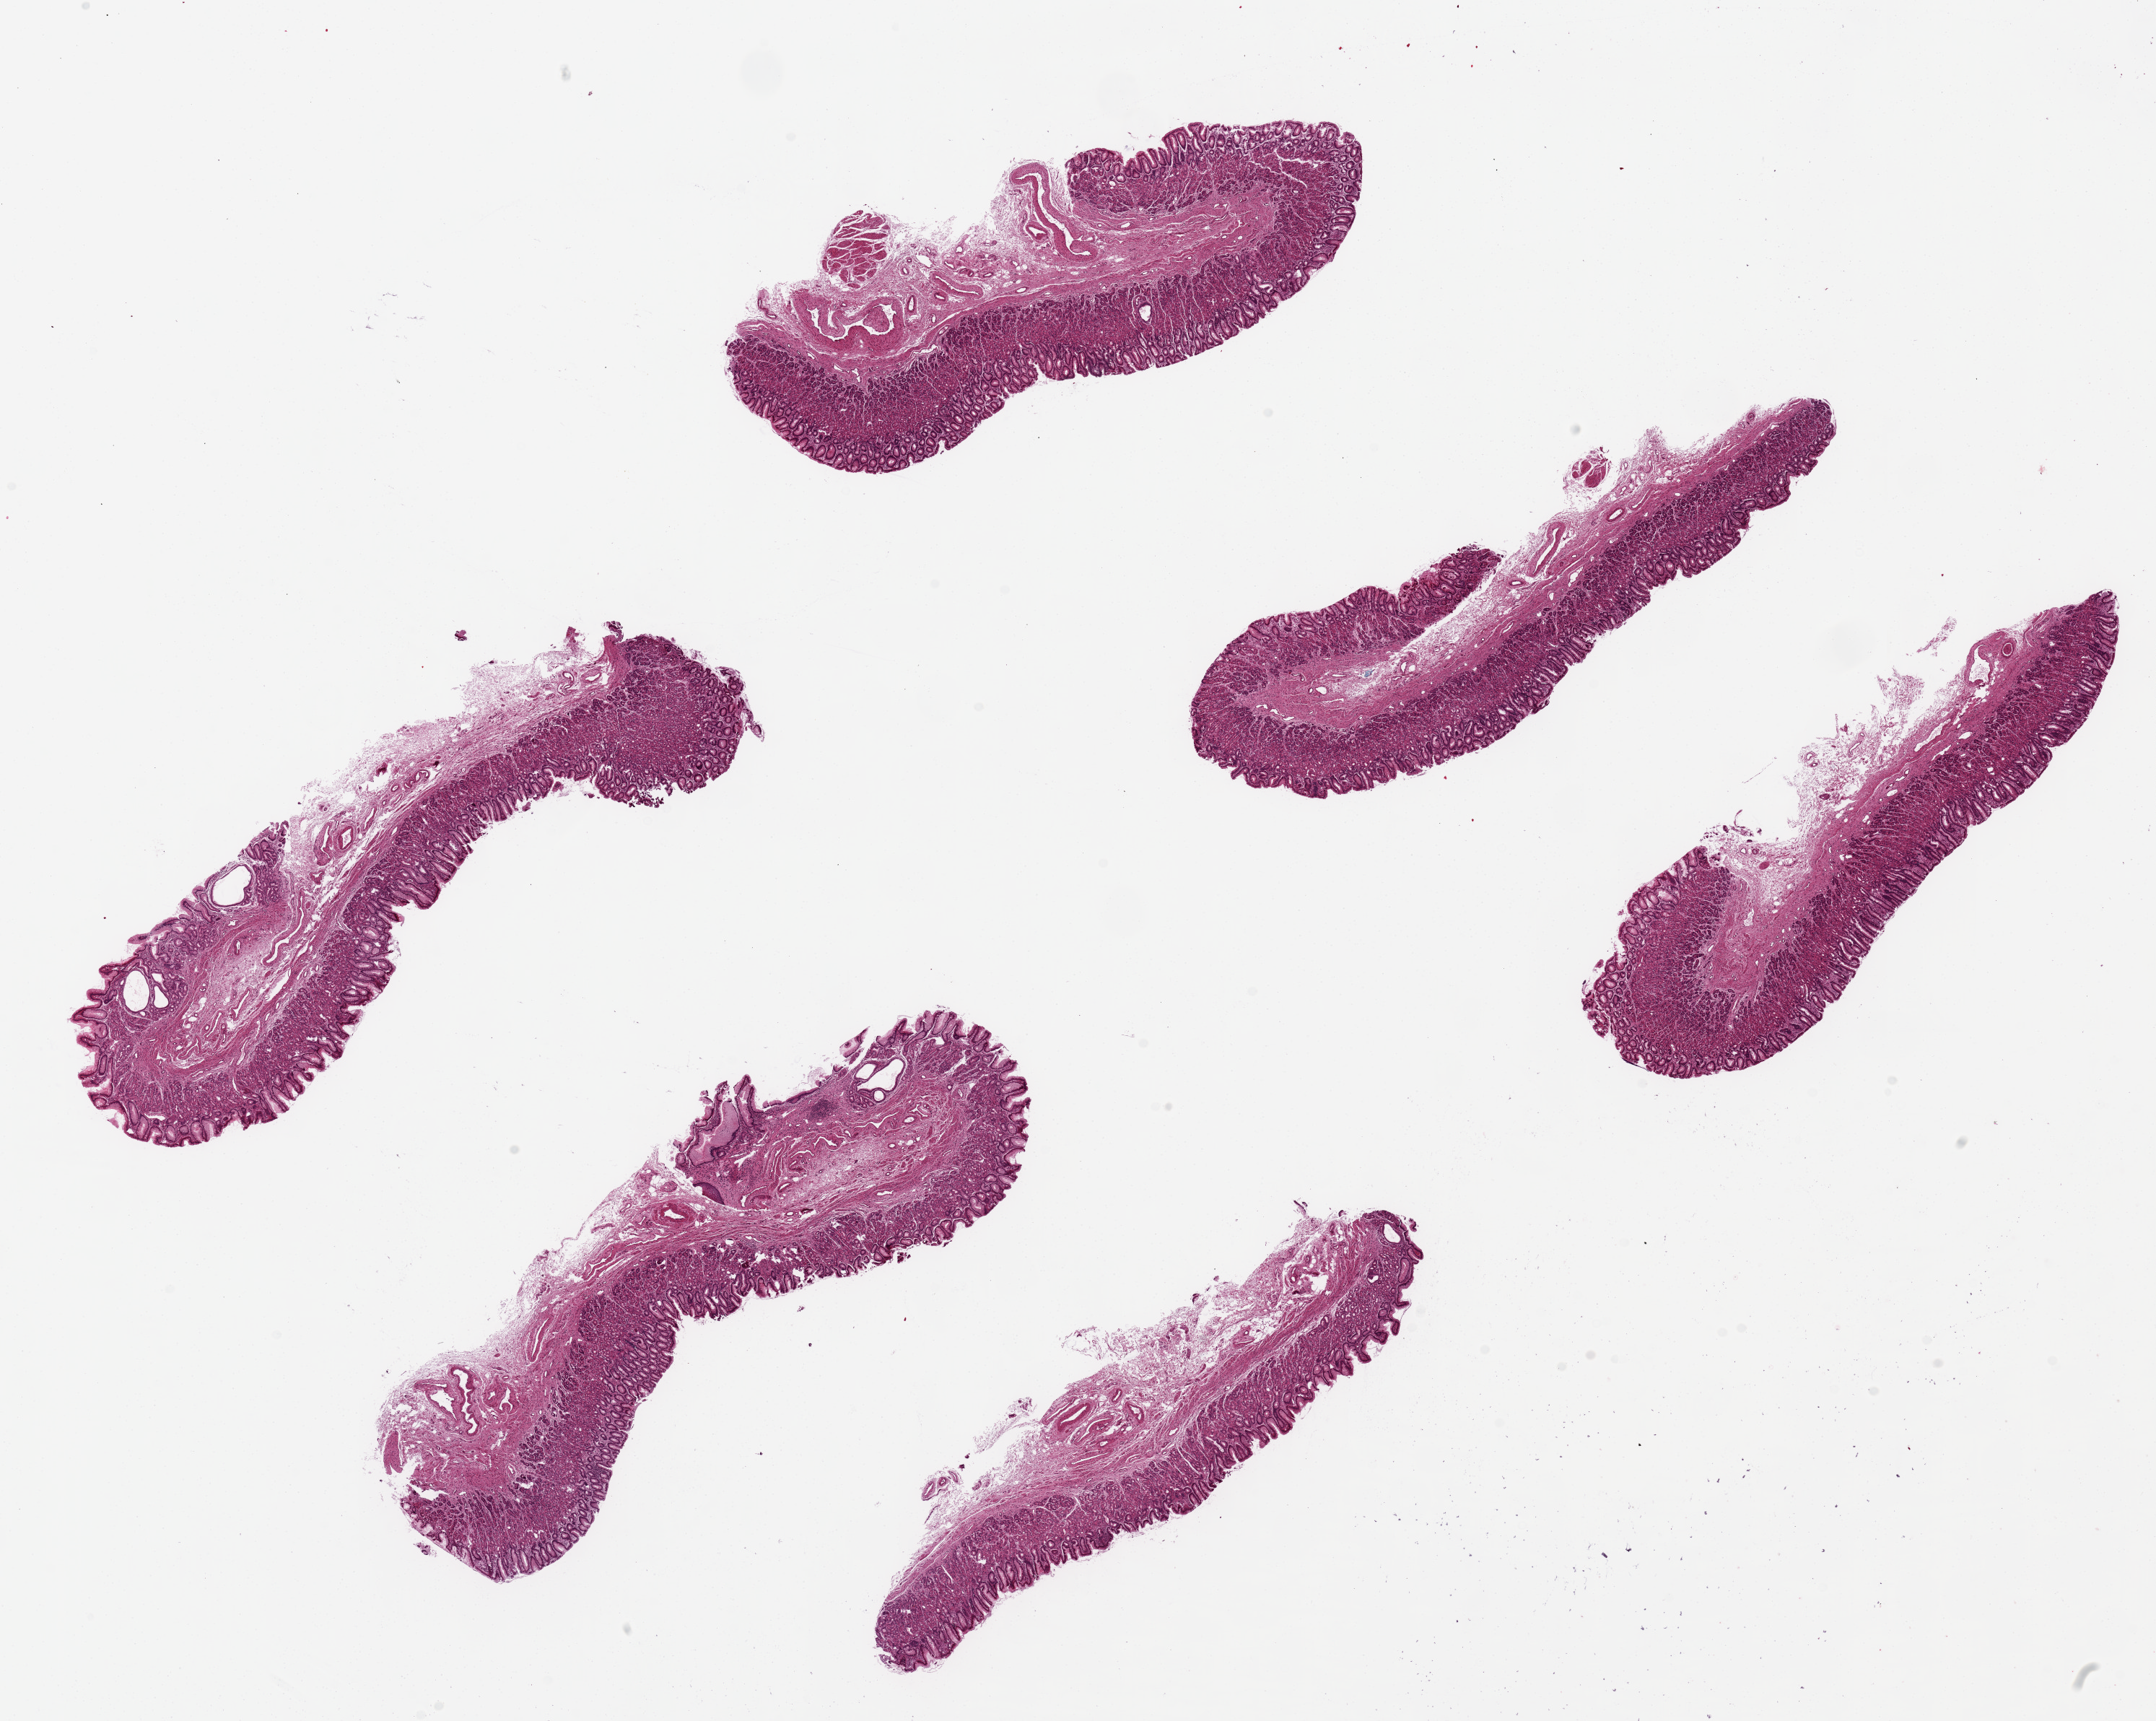
Digitized H&E-stained section, whole scanned area (about 23.6 x 18.9 mm) shown as a low-resolution overview. Donor sex: female.
Specimen: PAXgene-fixed, paraffin-embedded tissue; sampled site (target tissue): stomach; donor tissue sample.